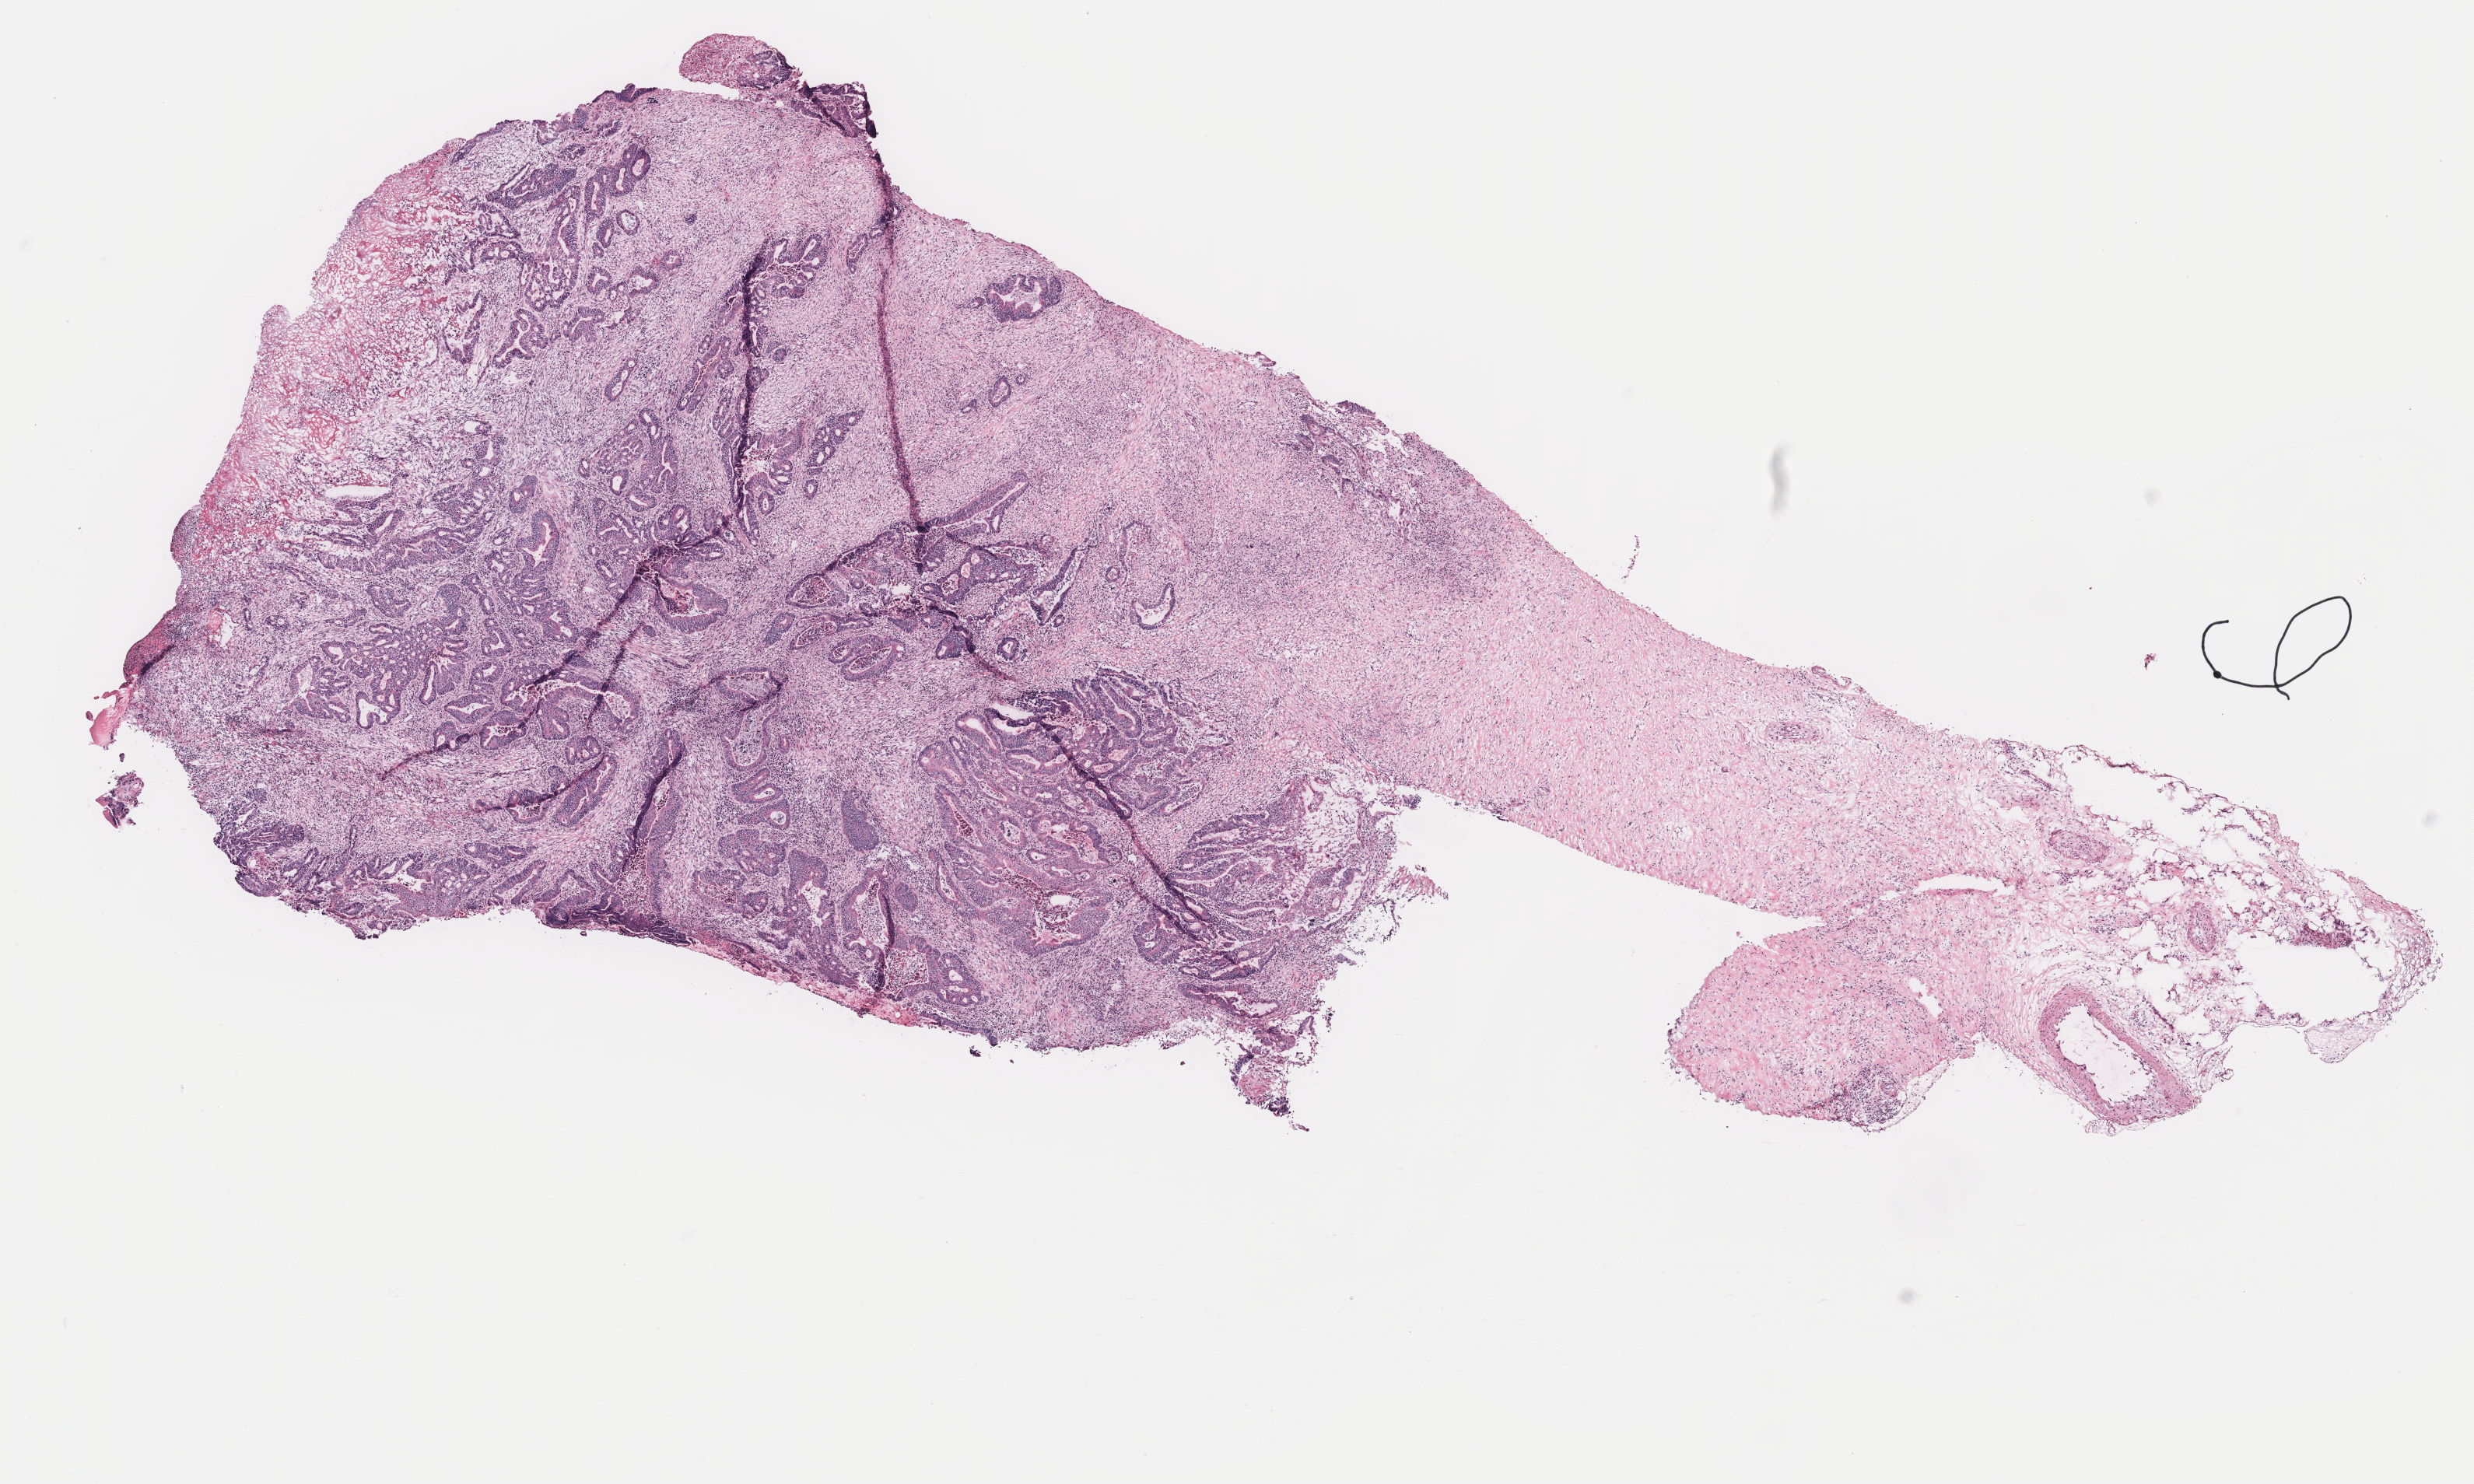
Hematoxylin and eosin (H&E) stained whole-slide image — low-resolution overview of the scanned area, about 12.7 x 7.6 mm (acquisition: 40x scan), colon, tissue type not recorded.
Patient diagnosis (cohort enrolment): colon cancer (colon).